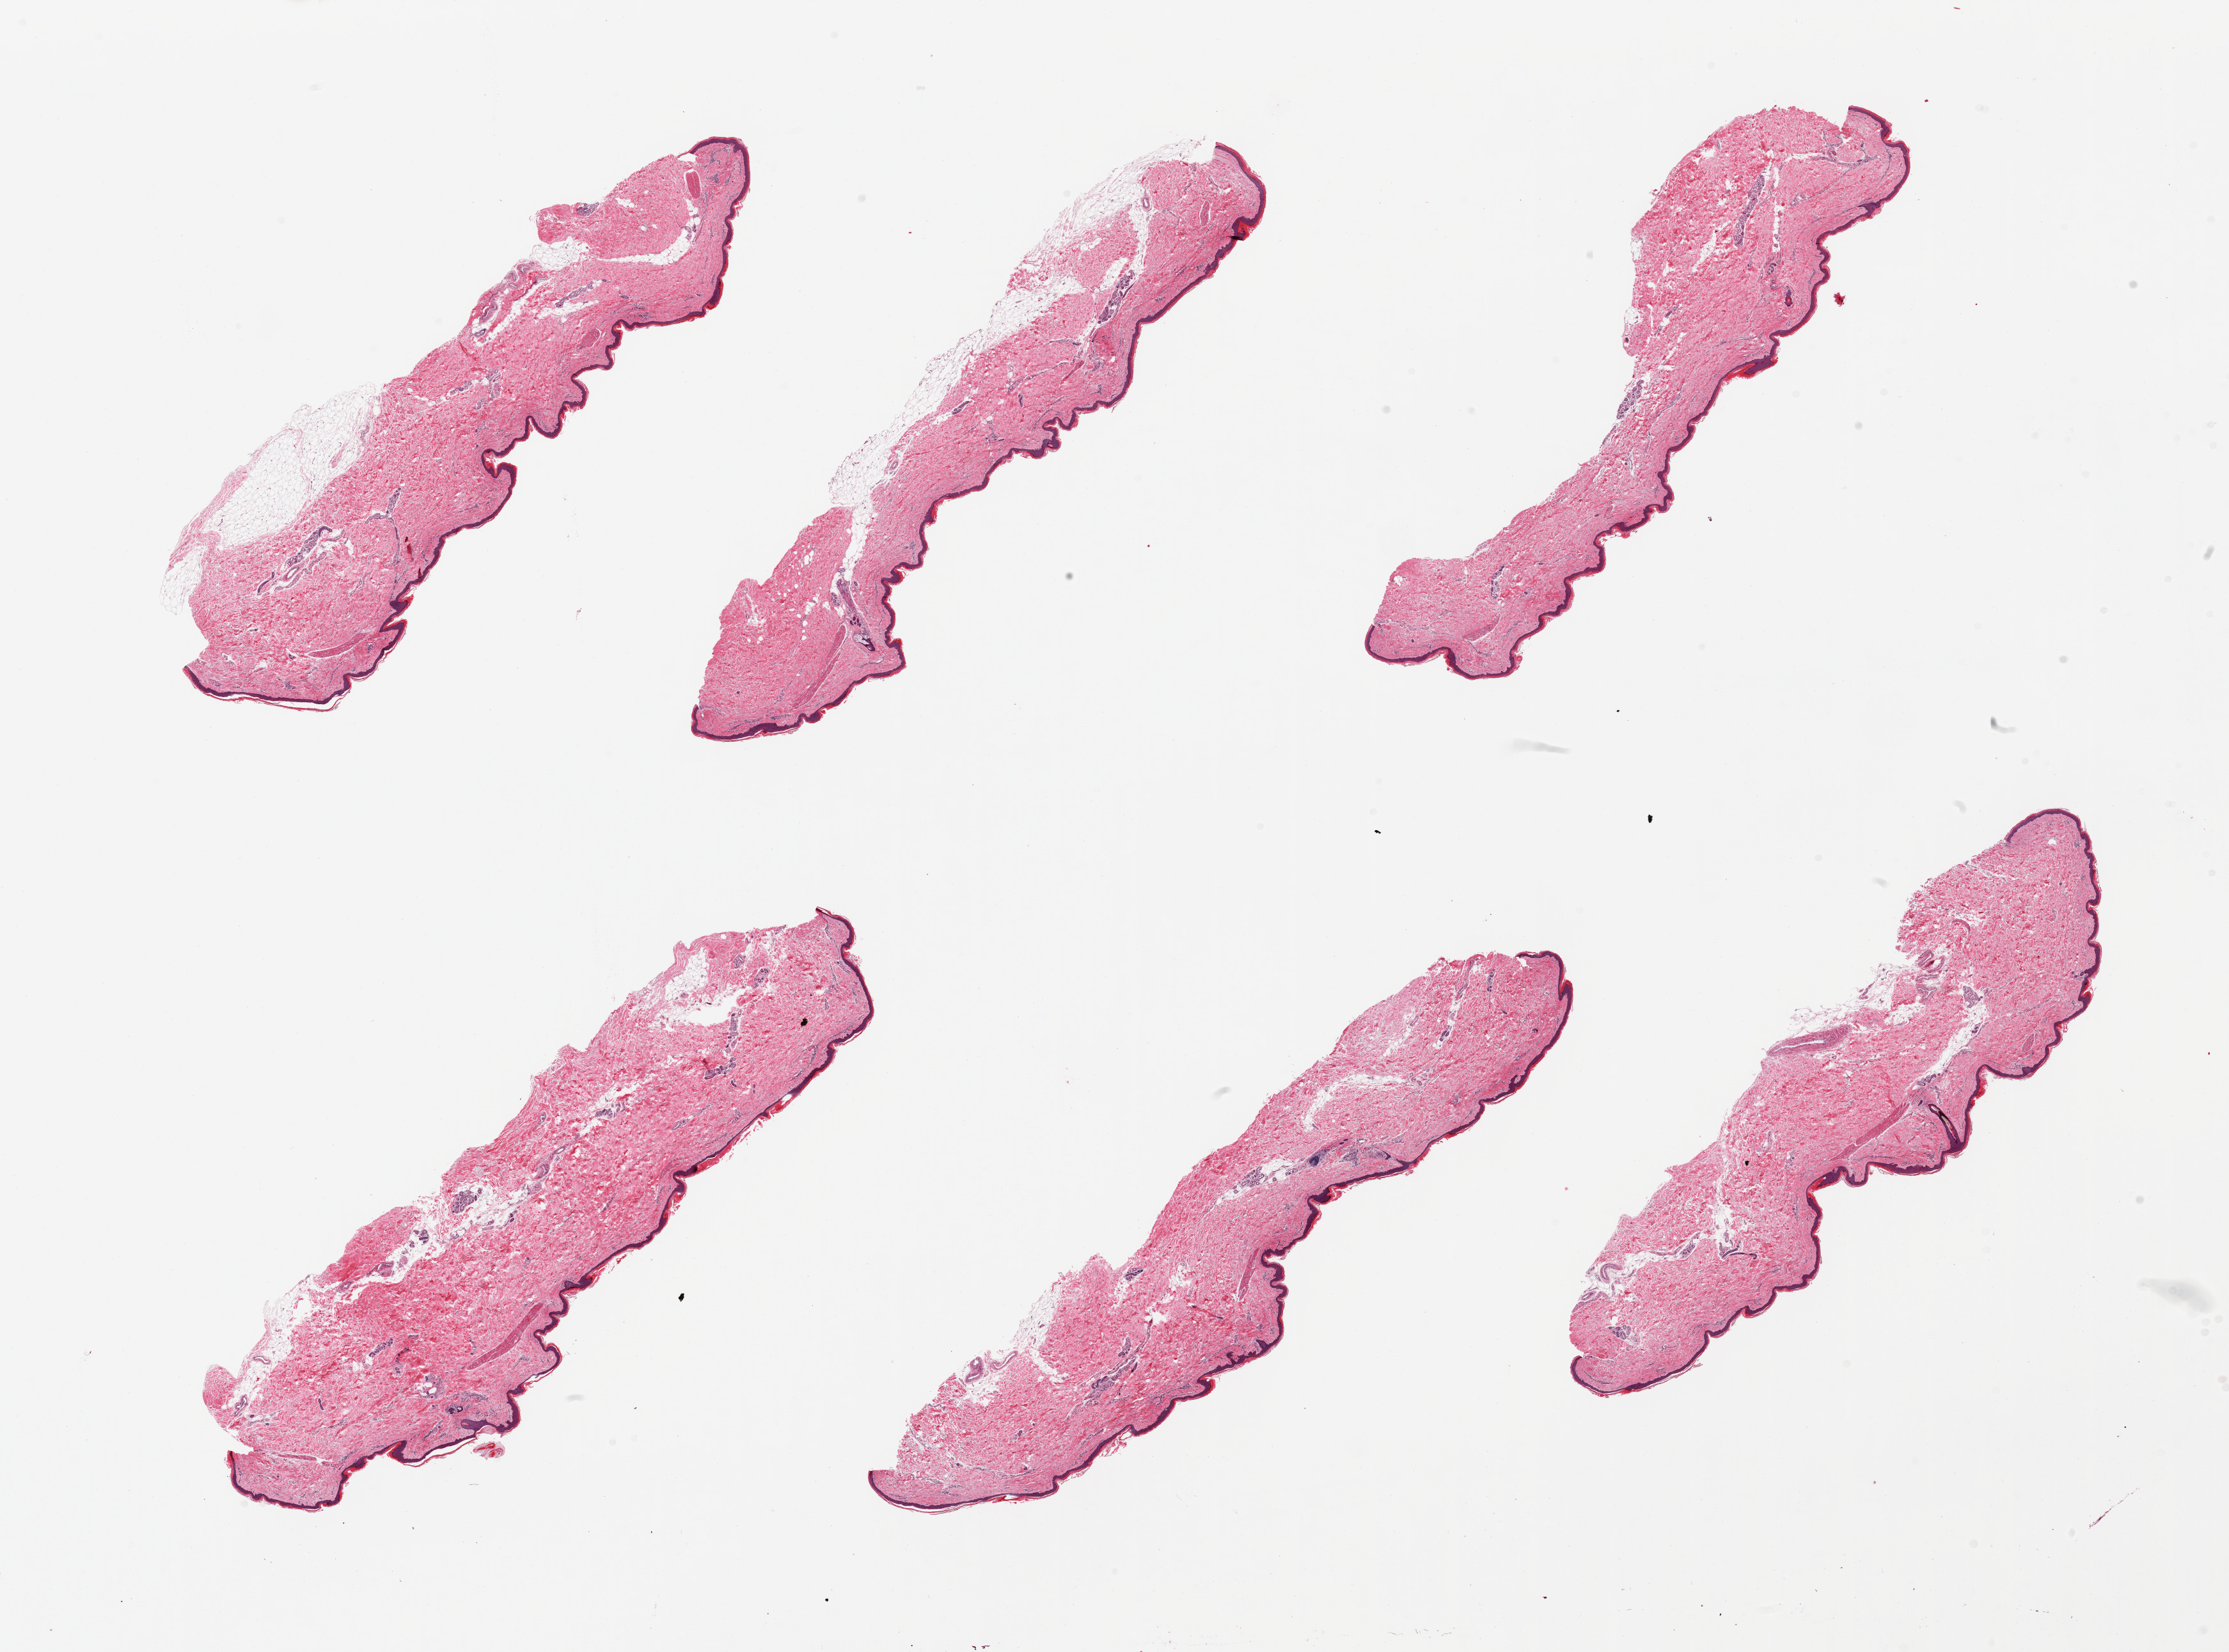
Haematoxylin and eosin whole-slide image, brightfield, low-resolution overview of the scanned area, about 27.6 x 20.4 mm (from a 20x scan). PAXgene-fixed paraffin-embedded (PFPE) section. Section of skin of lower leg (target tissue). Tissue donor sample. Donor sex: male.
Reviewer comment on this tissue sample: 6 pieces; few pieces include residual attached fat, up to 15%, epidermis measures 49 microns.